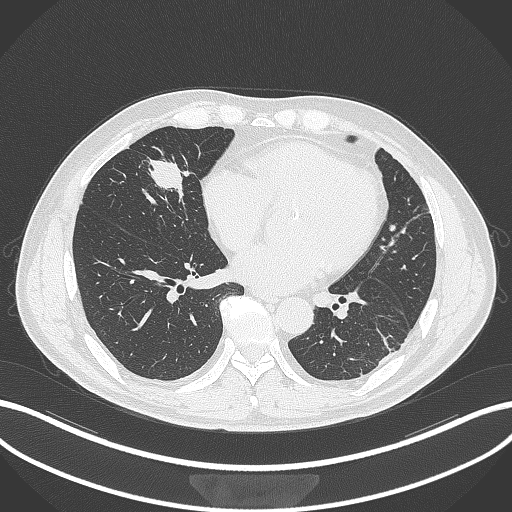
Chest CT, one axial slice; slice 109 of 399 in the series (ordered by position); reconstruction kernel B70f; lung window (W 1500 / L -600 HU); 1 mm slice thickness; 512 × 512 image matrix, field of view 400 × 400 mm. Patient: male, 59 years. Case-level facts recorded for this patient, not image findings: clinical TNM (as recorded): T2a N1 M0.
Annotated regions visible in this slice (bounding box drawn by a radiologist):
- lung tumour (recorded histology: adenocarcinoma): box from (x=140, y=150) to (x=192, y=204) px